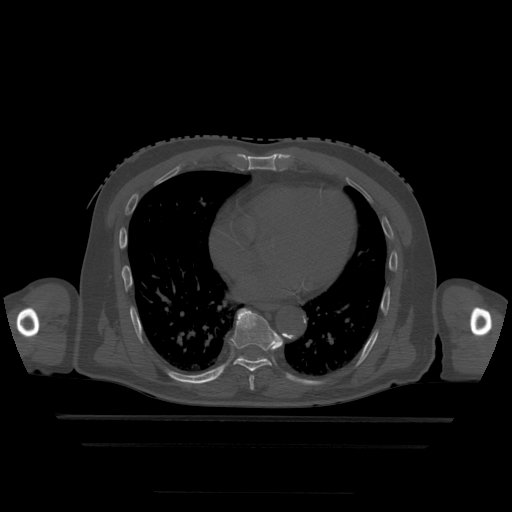
CT including the spine, one axial slice. Slice 278 of 522 in the series (ordered by position). Bone window (W 1800 / L 400 HU). 1.25 mm slice thickness. 512 × 512 image matrix, field of view 436 × 436 mm. Patient age 68 years. Case-level facts recorded for this patient, not image findings: primary cancer: urothelial.
Outlined on this slice (semi-automatic segmentation, software-assisted and operator-edited):
- T7 vertebra: box from (x=249, y=376) to (x=255, y=391) px
- T8 vertebra: (x=230, y=308)–(x=283, y=372)
- T9 vertebra: (x=238, y=356)–(x=267, y=361)